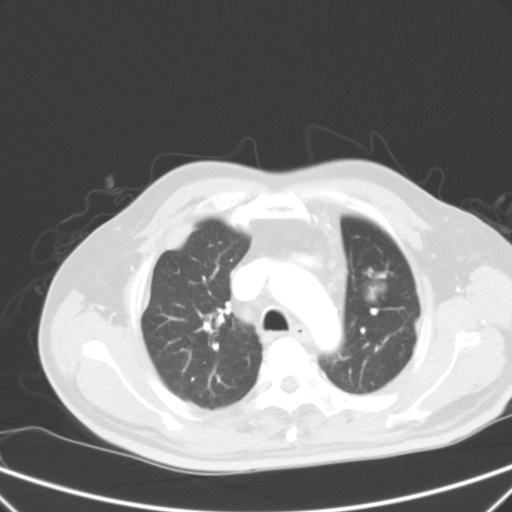
Chest CT, one axial slice; slice 44 of 59 in the series (ordered by position); intravenous contrast given; lung window (W 1500 / L -600 HU); 5 mm slice thickness; 512 × 512 image matrix. Patient: male, 66 years. Case-level facts recorded for this patient, not image findings: clinical TNM (as recorded): T1c N3 M1a.
Structures marked on this image (bounding box drawn by a radiologist):
- lung tumour (recorded histology: squamous cell carcinoma): bounding box (x1, y1, x2, y2) in pixels: (361, 264, 394, 308)